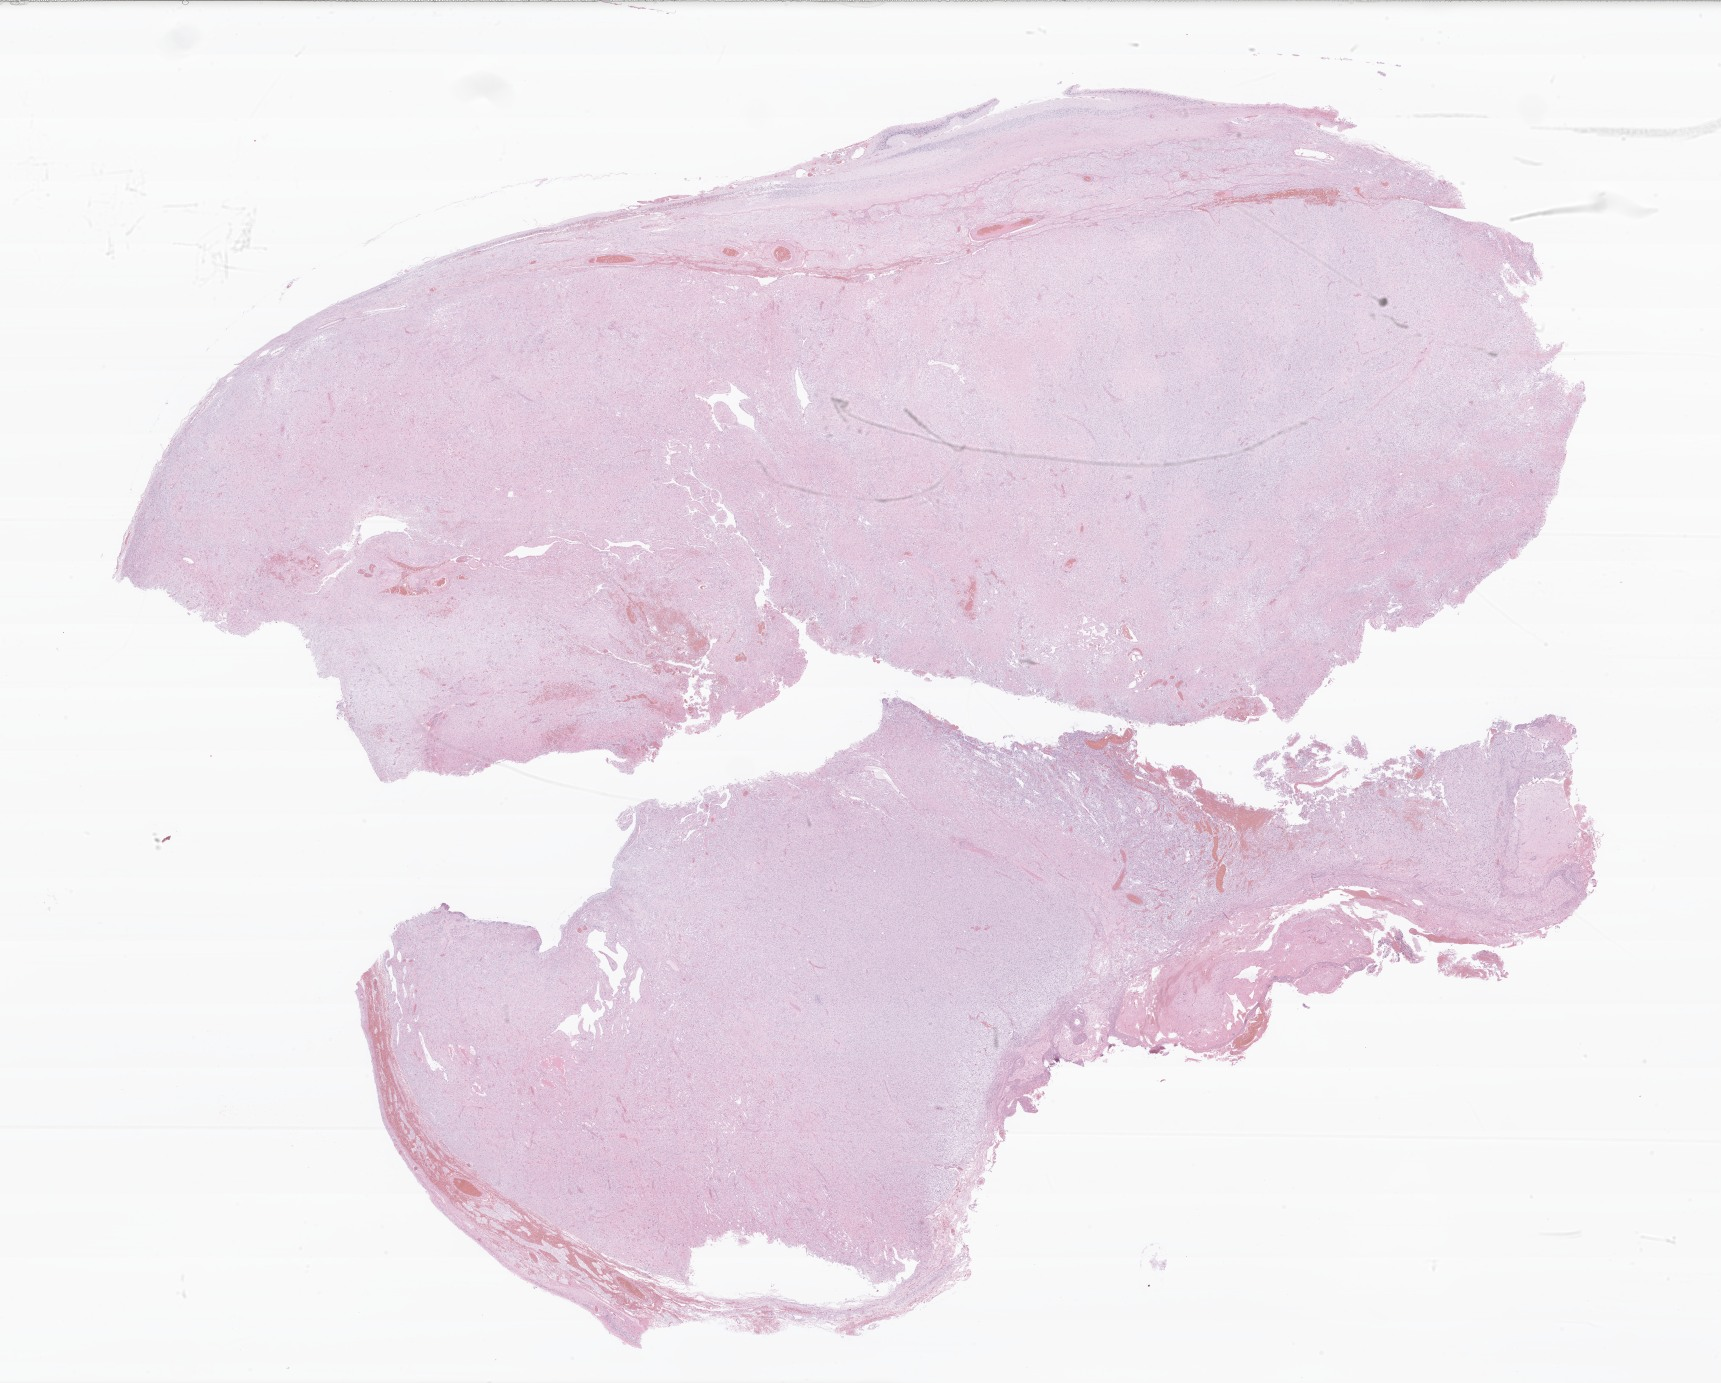
Haematoxylin and eosin whole-slide image of tumor tissue from the brain, a low-resolution overview of the entire scanned area, about 28.9 x 23.3 mm, FFPE section. Patient female; age 130 months.
Diagnosis (ICD-O-3 morphology term): Pilocytic astrocytoma.